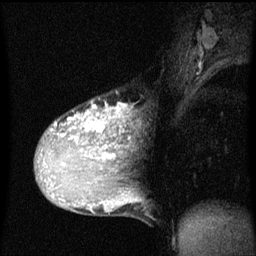
Breast MRI (dynamic contrast-enhanced), one sagittal slice. Slice 34 of 60 in the series (ordered by position). Dynamic contrast-enhanced series, image 2 of 3 at this slice position (ordered by acquisition). 1.5 T. TE 4.2 ms, TR 8 ms. 256 × 256 image matrix. Patient: female, 36 years.
Structures marked on this image (semi-automatic segmentation, software-assisted and operator-edited):
- analysis volume of interest (the breast-tissue region the enhancement analysis was run in; not a lesion): bounding box [x1, y1, x2, y2] px = [35, 102, 128, 169]
- tumour enhancement mask (voxels above the 70 % enhancement threshold inside the analysis volume of interest): [52, 102, 127, 163]